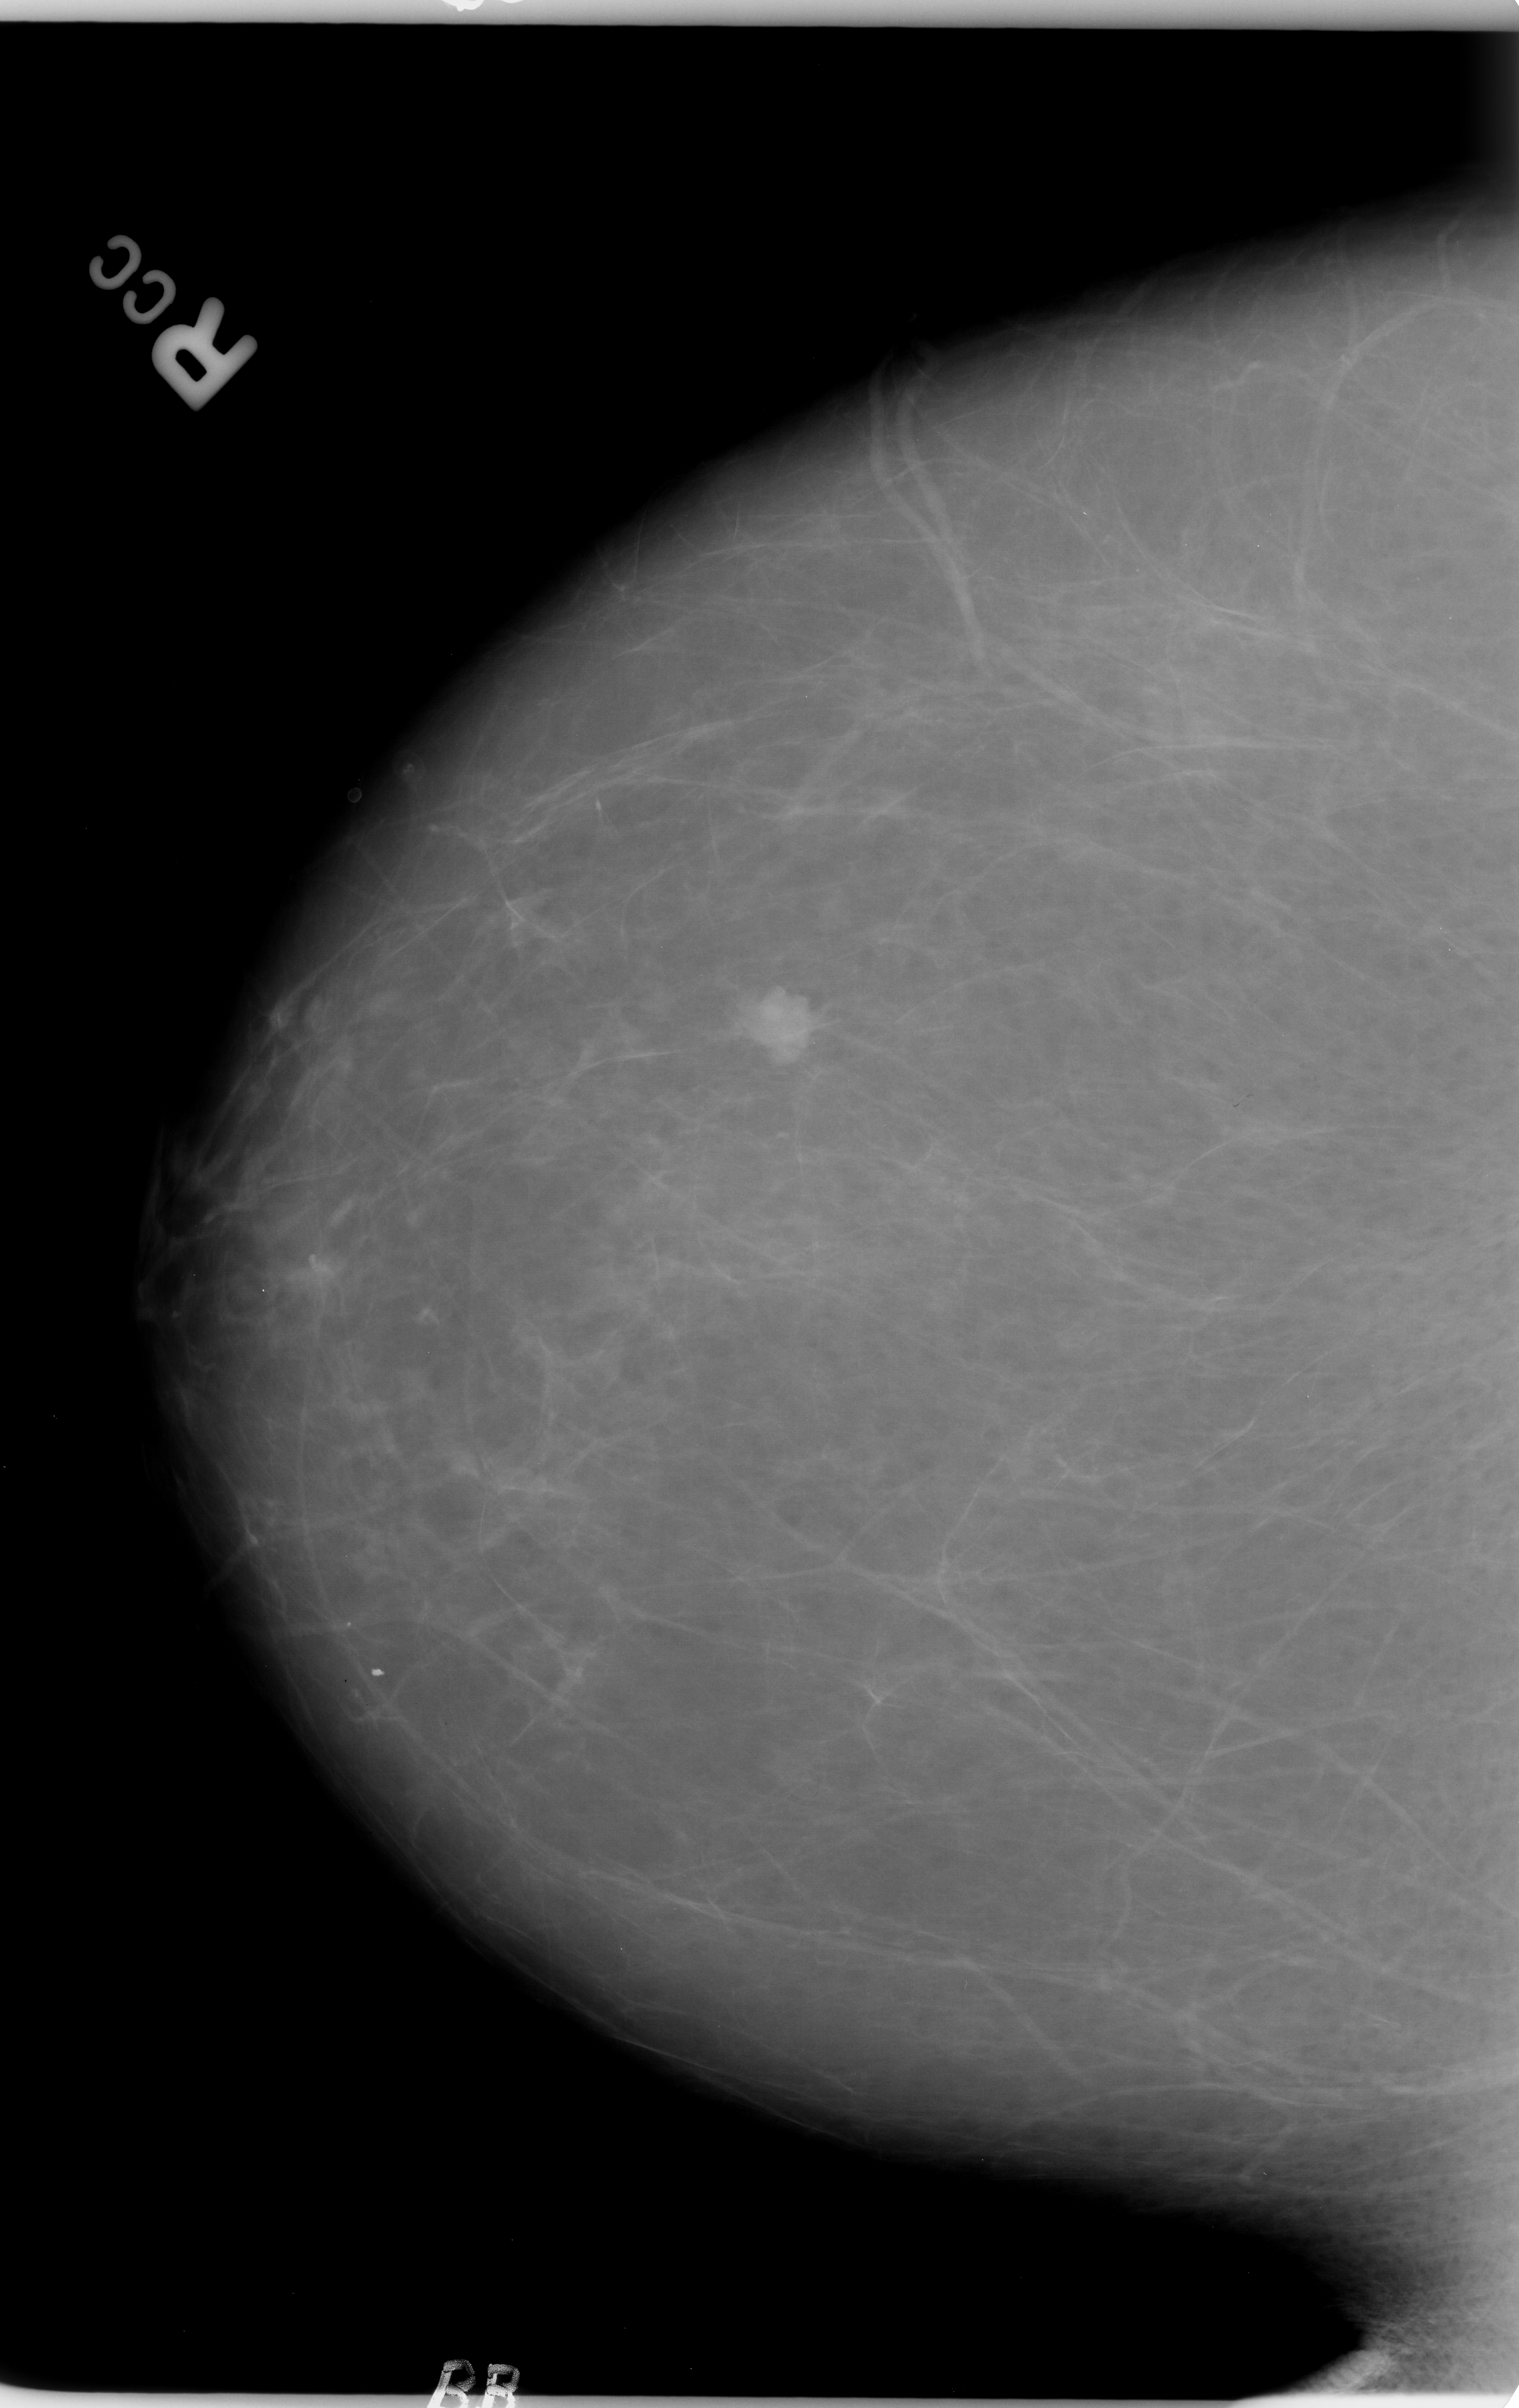
Digitized screen-film mammogram; right breast; craniocaudal (CC) view.
- Finding: mass, shape lobulated, margins circumscribed / ill defined; BI-RADS assessment category 4; pathology result (as recorded, not read from the image): benign.